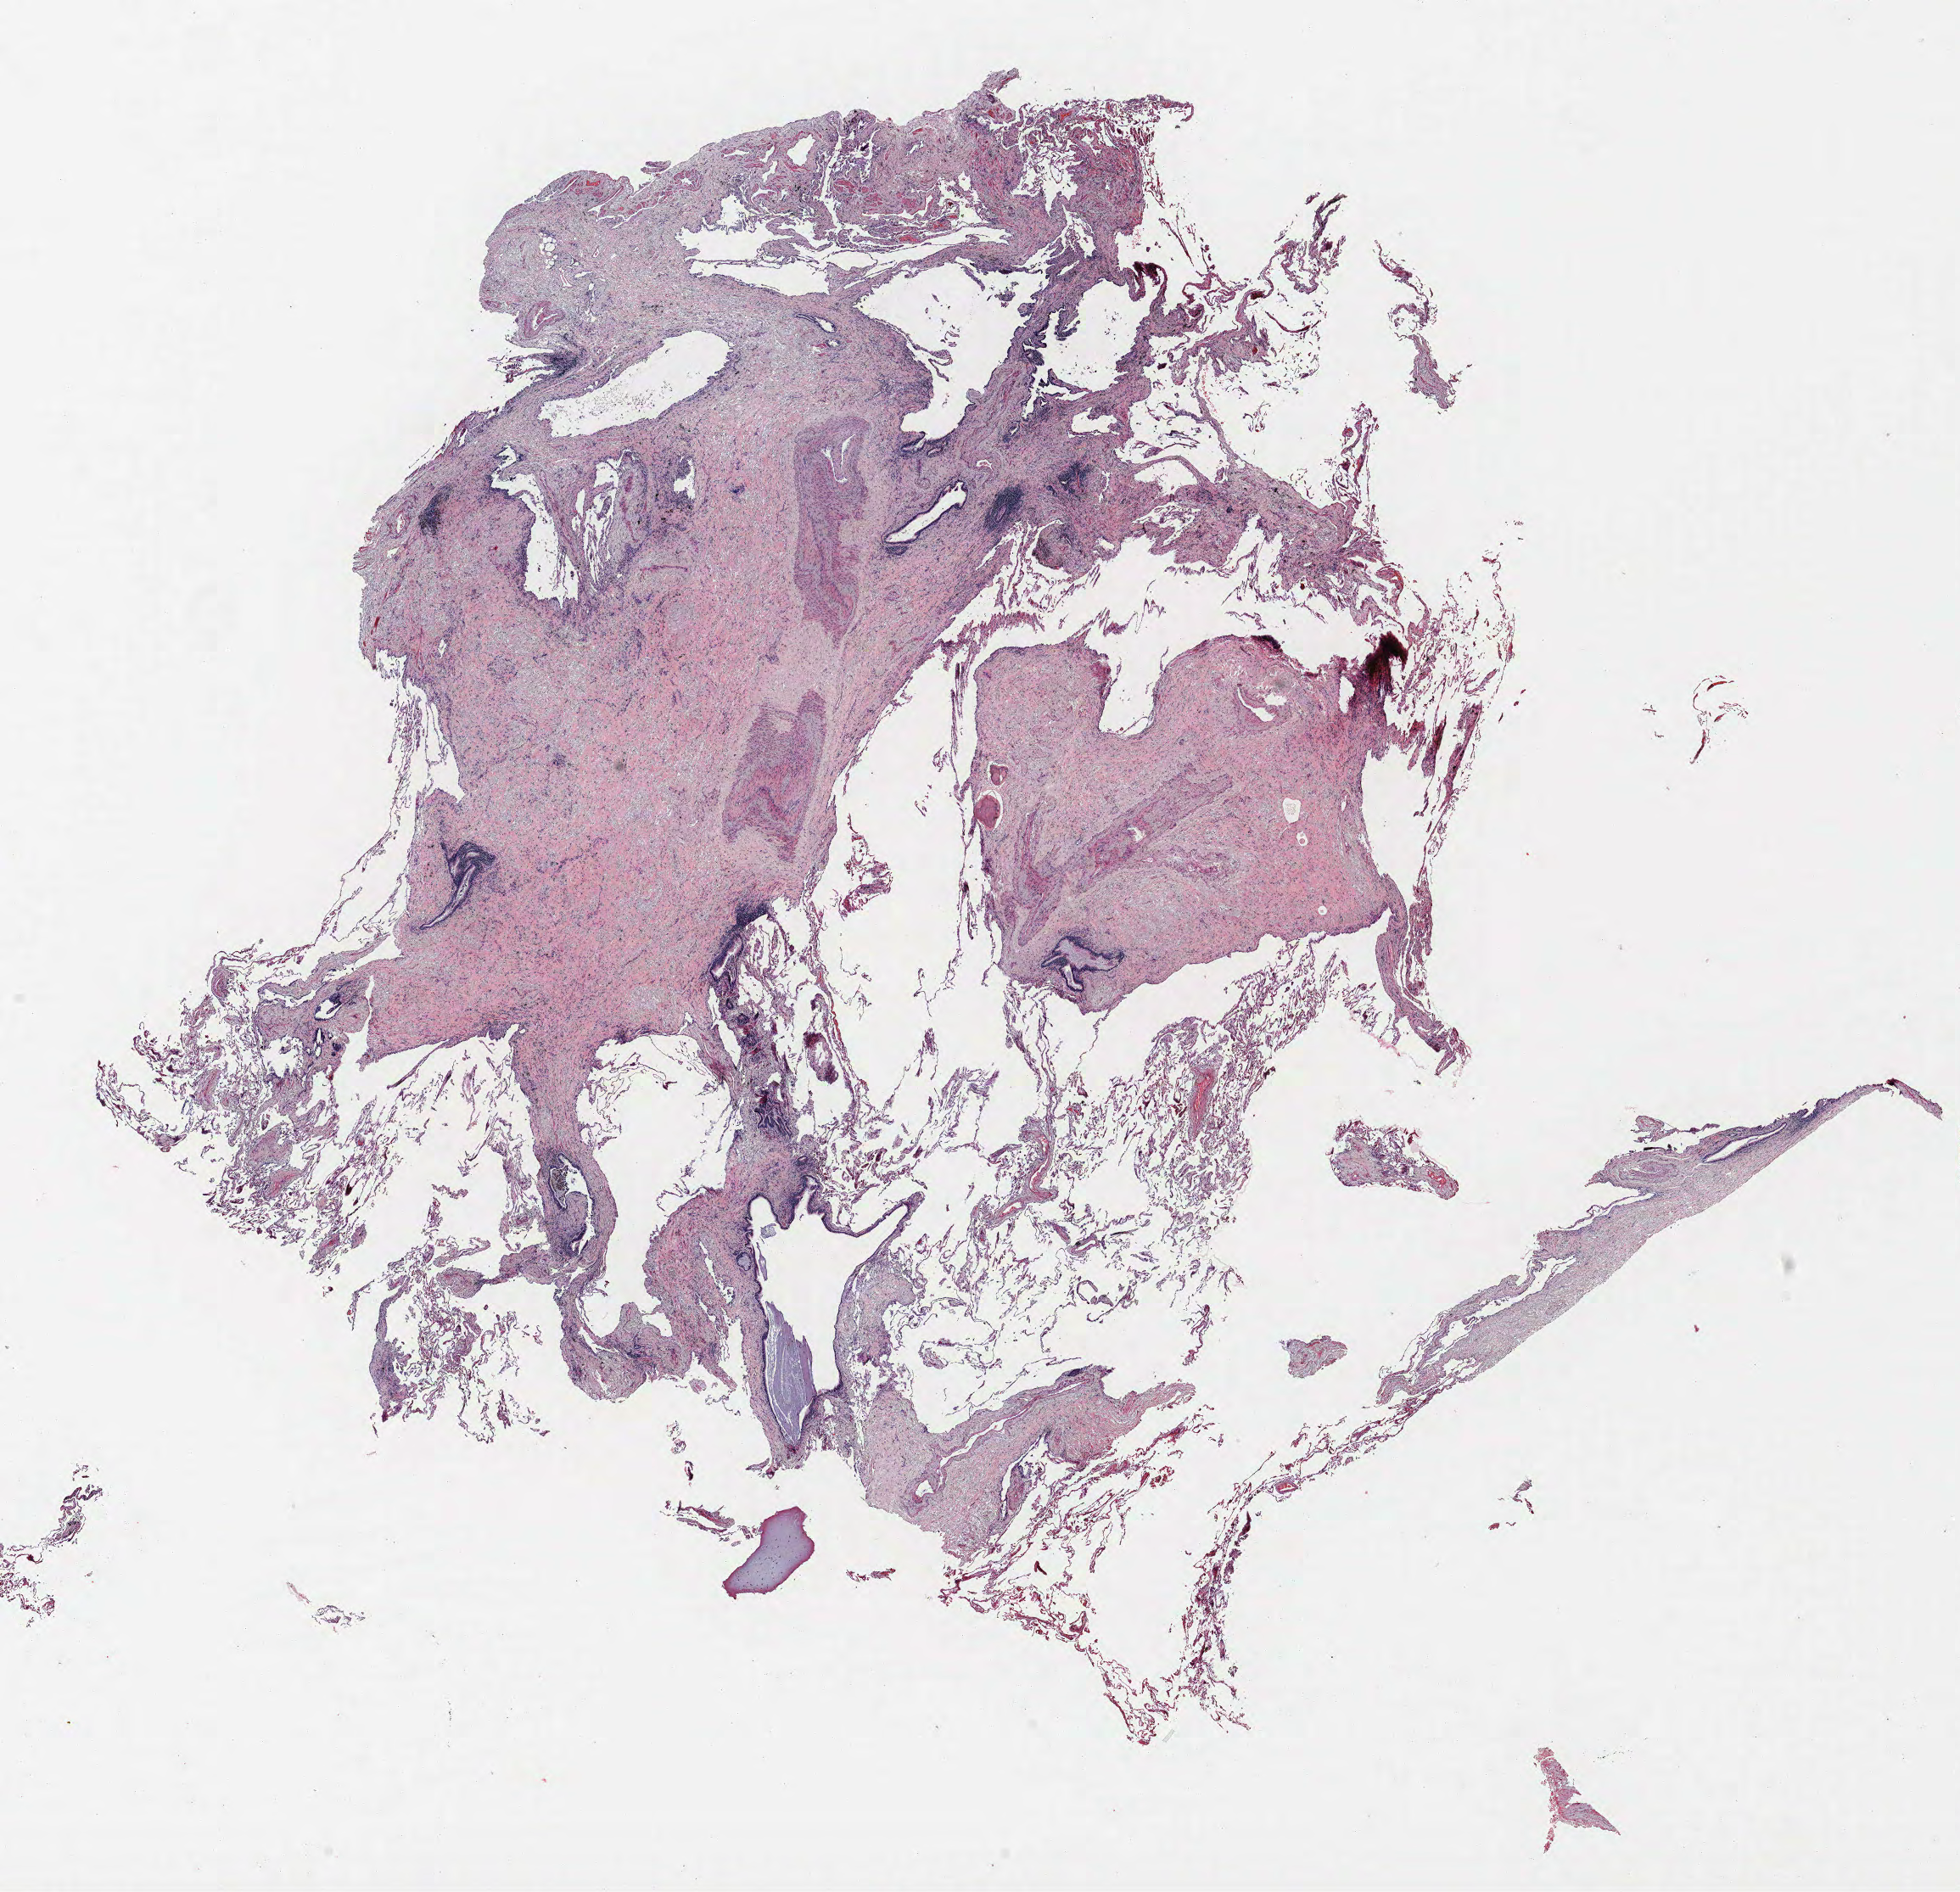
H&E whole-slide image, low-resolution overview of the scanned area, about 18.5 x 17.8 mm, FFPE section, lung tissue. Male patient, aged 65 at enrolment. Former smoker at enrolment.
Participant's lung-cancer diagnosis: Adenocarcinoma, NOS.